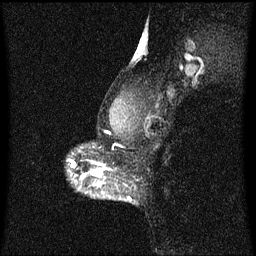
Breast MRI (dynamic contrast-enhanced), one sagittal slice; position 47 of 60 along the scan axis; dynamic contrast-enhanced series, image 2 of 3 at this slice position (ordered by acquisition); 1.5 T; TE 4.2 ms, TR 8.4 ms; 256 × 256 image matrix. Patient: female, 40 years.
Annotated regions visible in this slice (semi-automatically segmented with operator editing):
- analysis volume of interest (the breast-tissue region the enhancement analysis was run in; not a lesion): bounding box (x1, y1, x2, y2) in pixels: (76, 172, 104, 189)
- tumour enhancement mask (voxels above the 70 % enhancement threshold inside the analysis volume of interest): (83, 172, 103, 187)